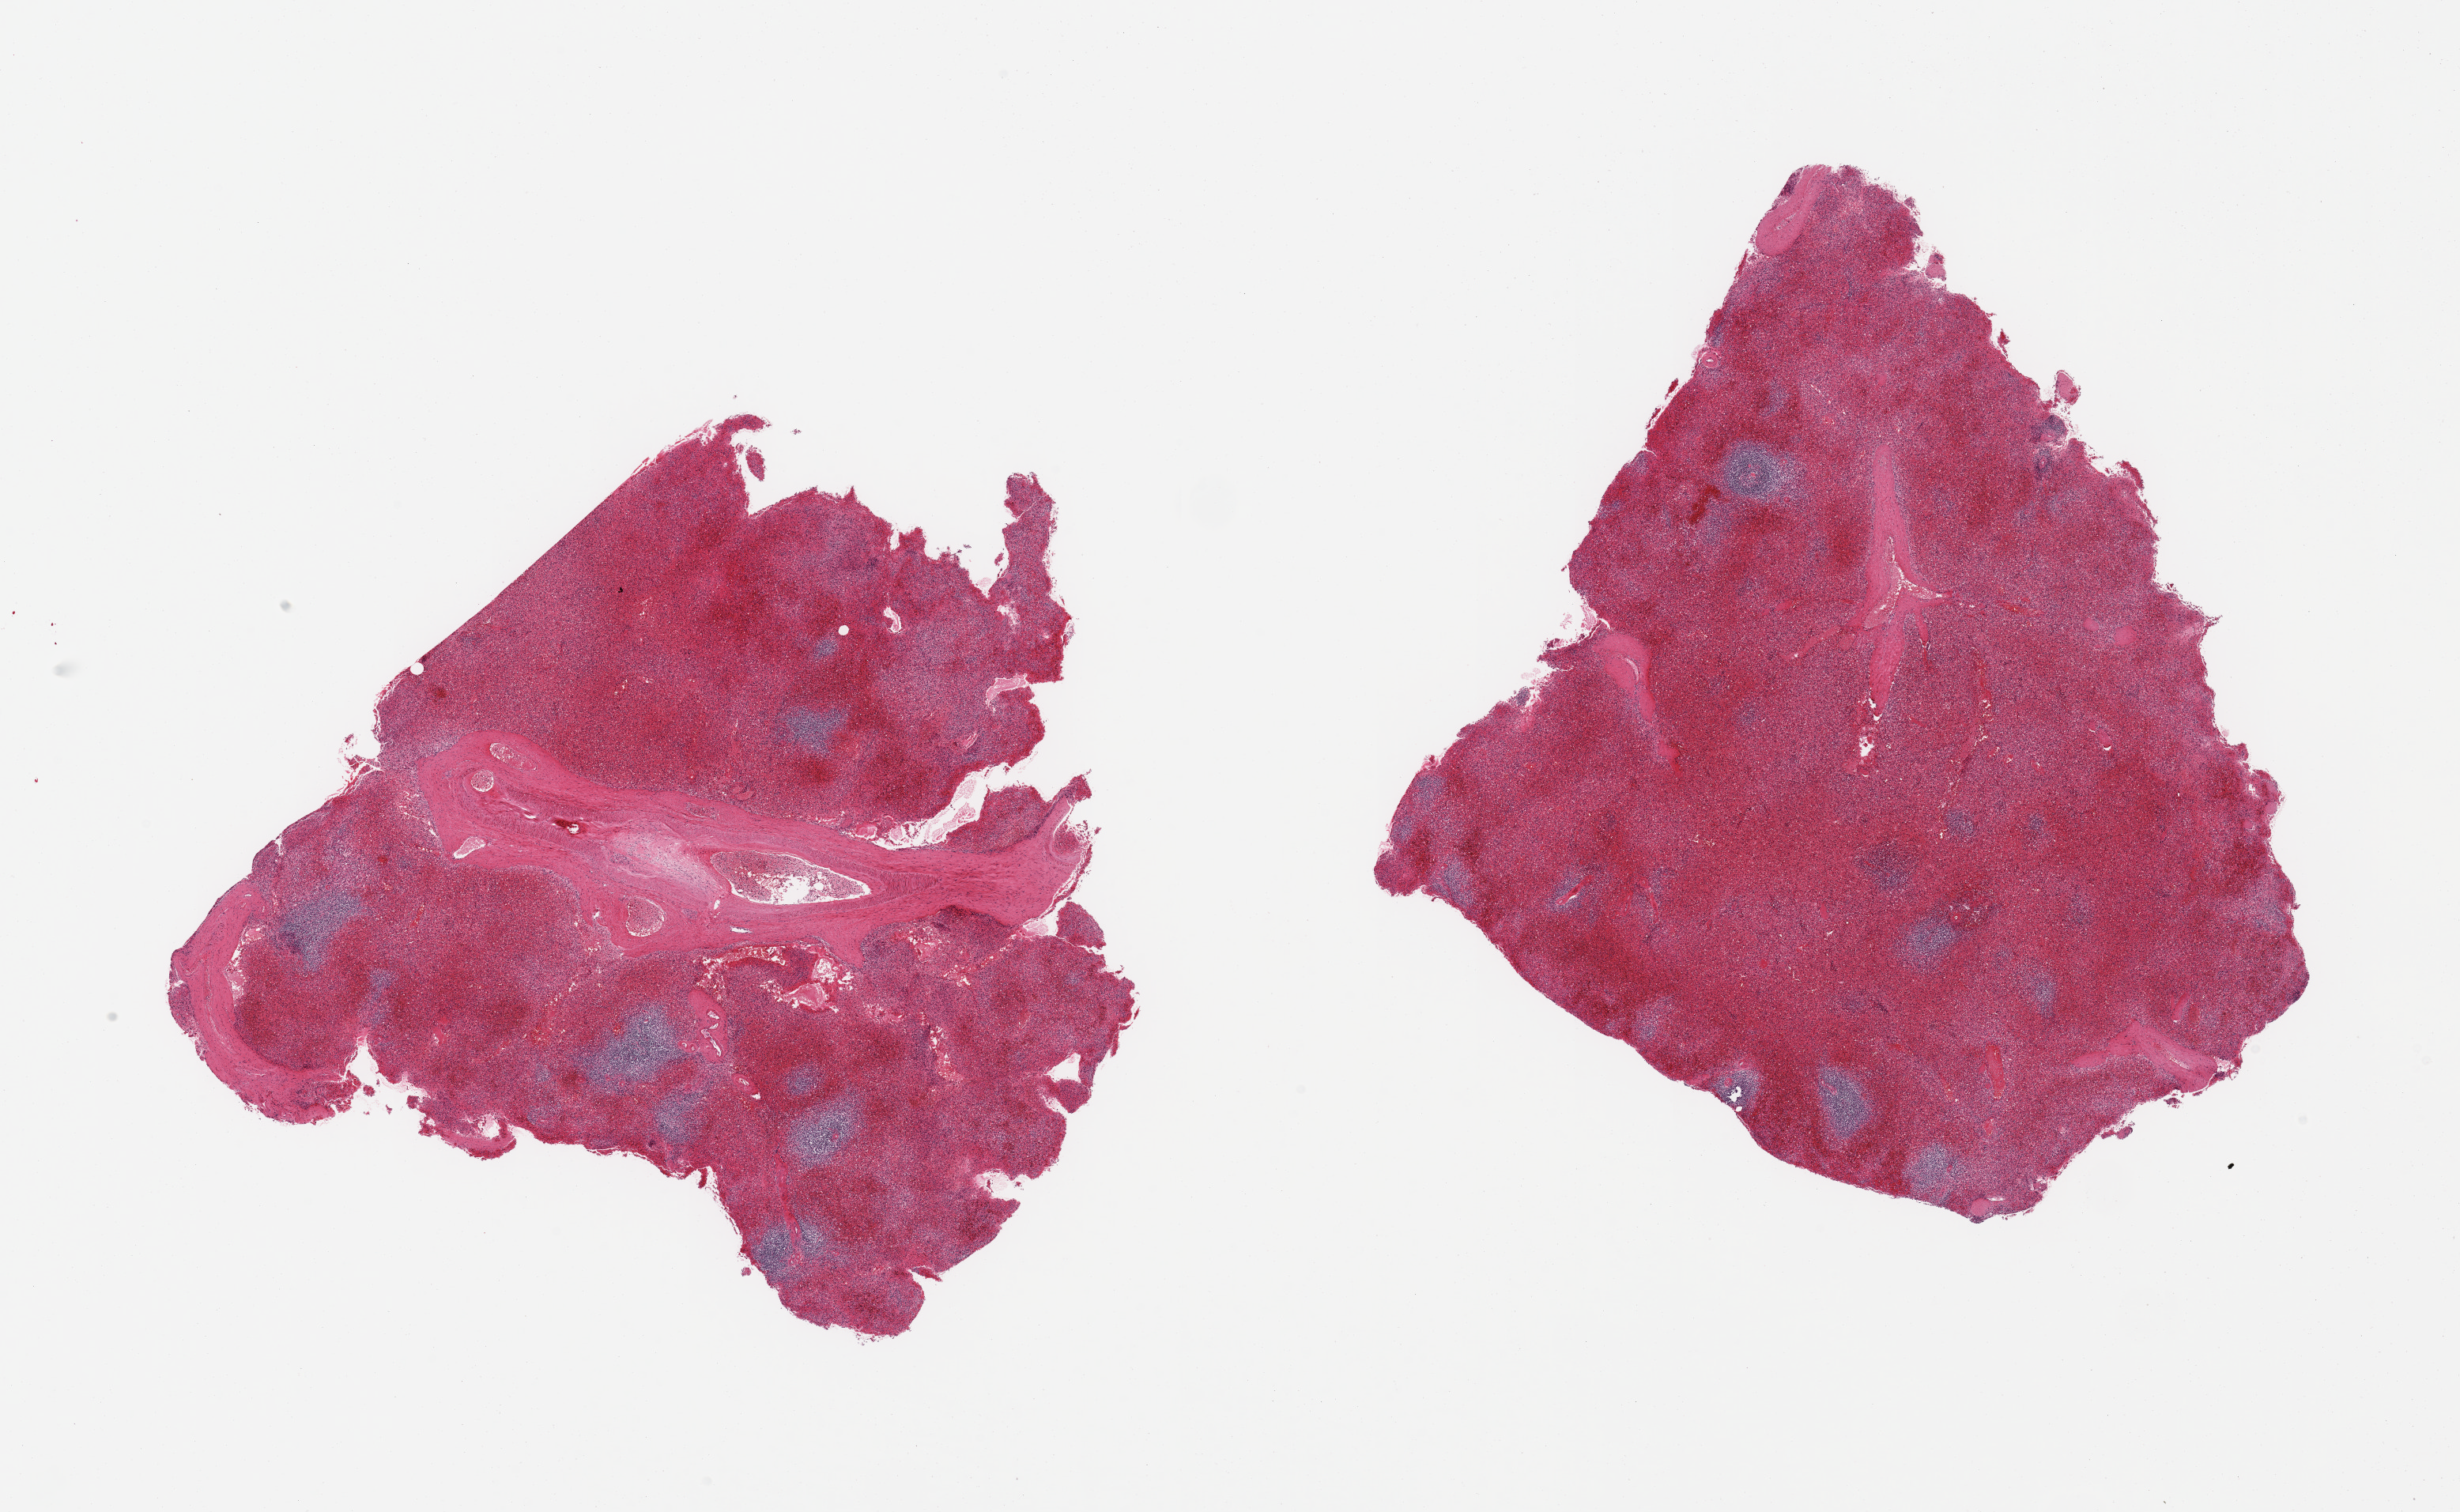
Digitized hematoxylin and eosin (H&E)-stained section, brightfield, a low-resolution overview of the entire scanned area, about 24.6 x 15.1 mm. PAXgene-fixed, paraffin-embedded tissue. Target tissue: spleen. Tissue donor sample. Donor: male.
- pathologist's review note for this sample: 2 pieces; congestion; one piece contains large, thick walled vessles